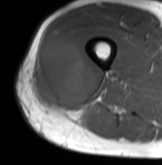
MRI of an extremity soft-tissue mass, one axial slice. Slice 35 of 61 in the series (ordered by position). MR volume resampled by the dataset authors to the PET/CT grid (not the native acquisition matrix). 3.27 mm slice thickness. 162 × 165 image matrix, field of view 158 × 161 mm. Male patient. Case-level facts recorded for this patient, not image findings: histological type: poorly differentiated synovial sarcoma; grade: high; site of the primary tumour: right buttock.
Annotated regions visible in this slice (expert contour drawn on MRI and transferred to this co-registered scan by the dataset authors):
- gross tumour volume including surrounding oedema: bounding box <34,36,97,112> (left, top, right, bottom; pixels)
- gross tumour volume (mass): <36,36,97,112>